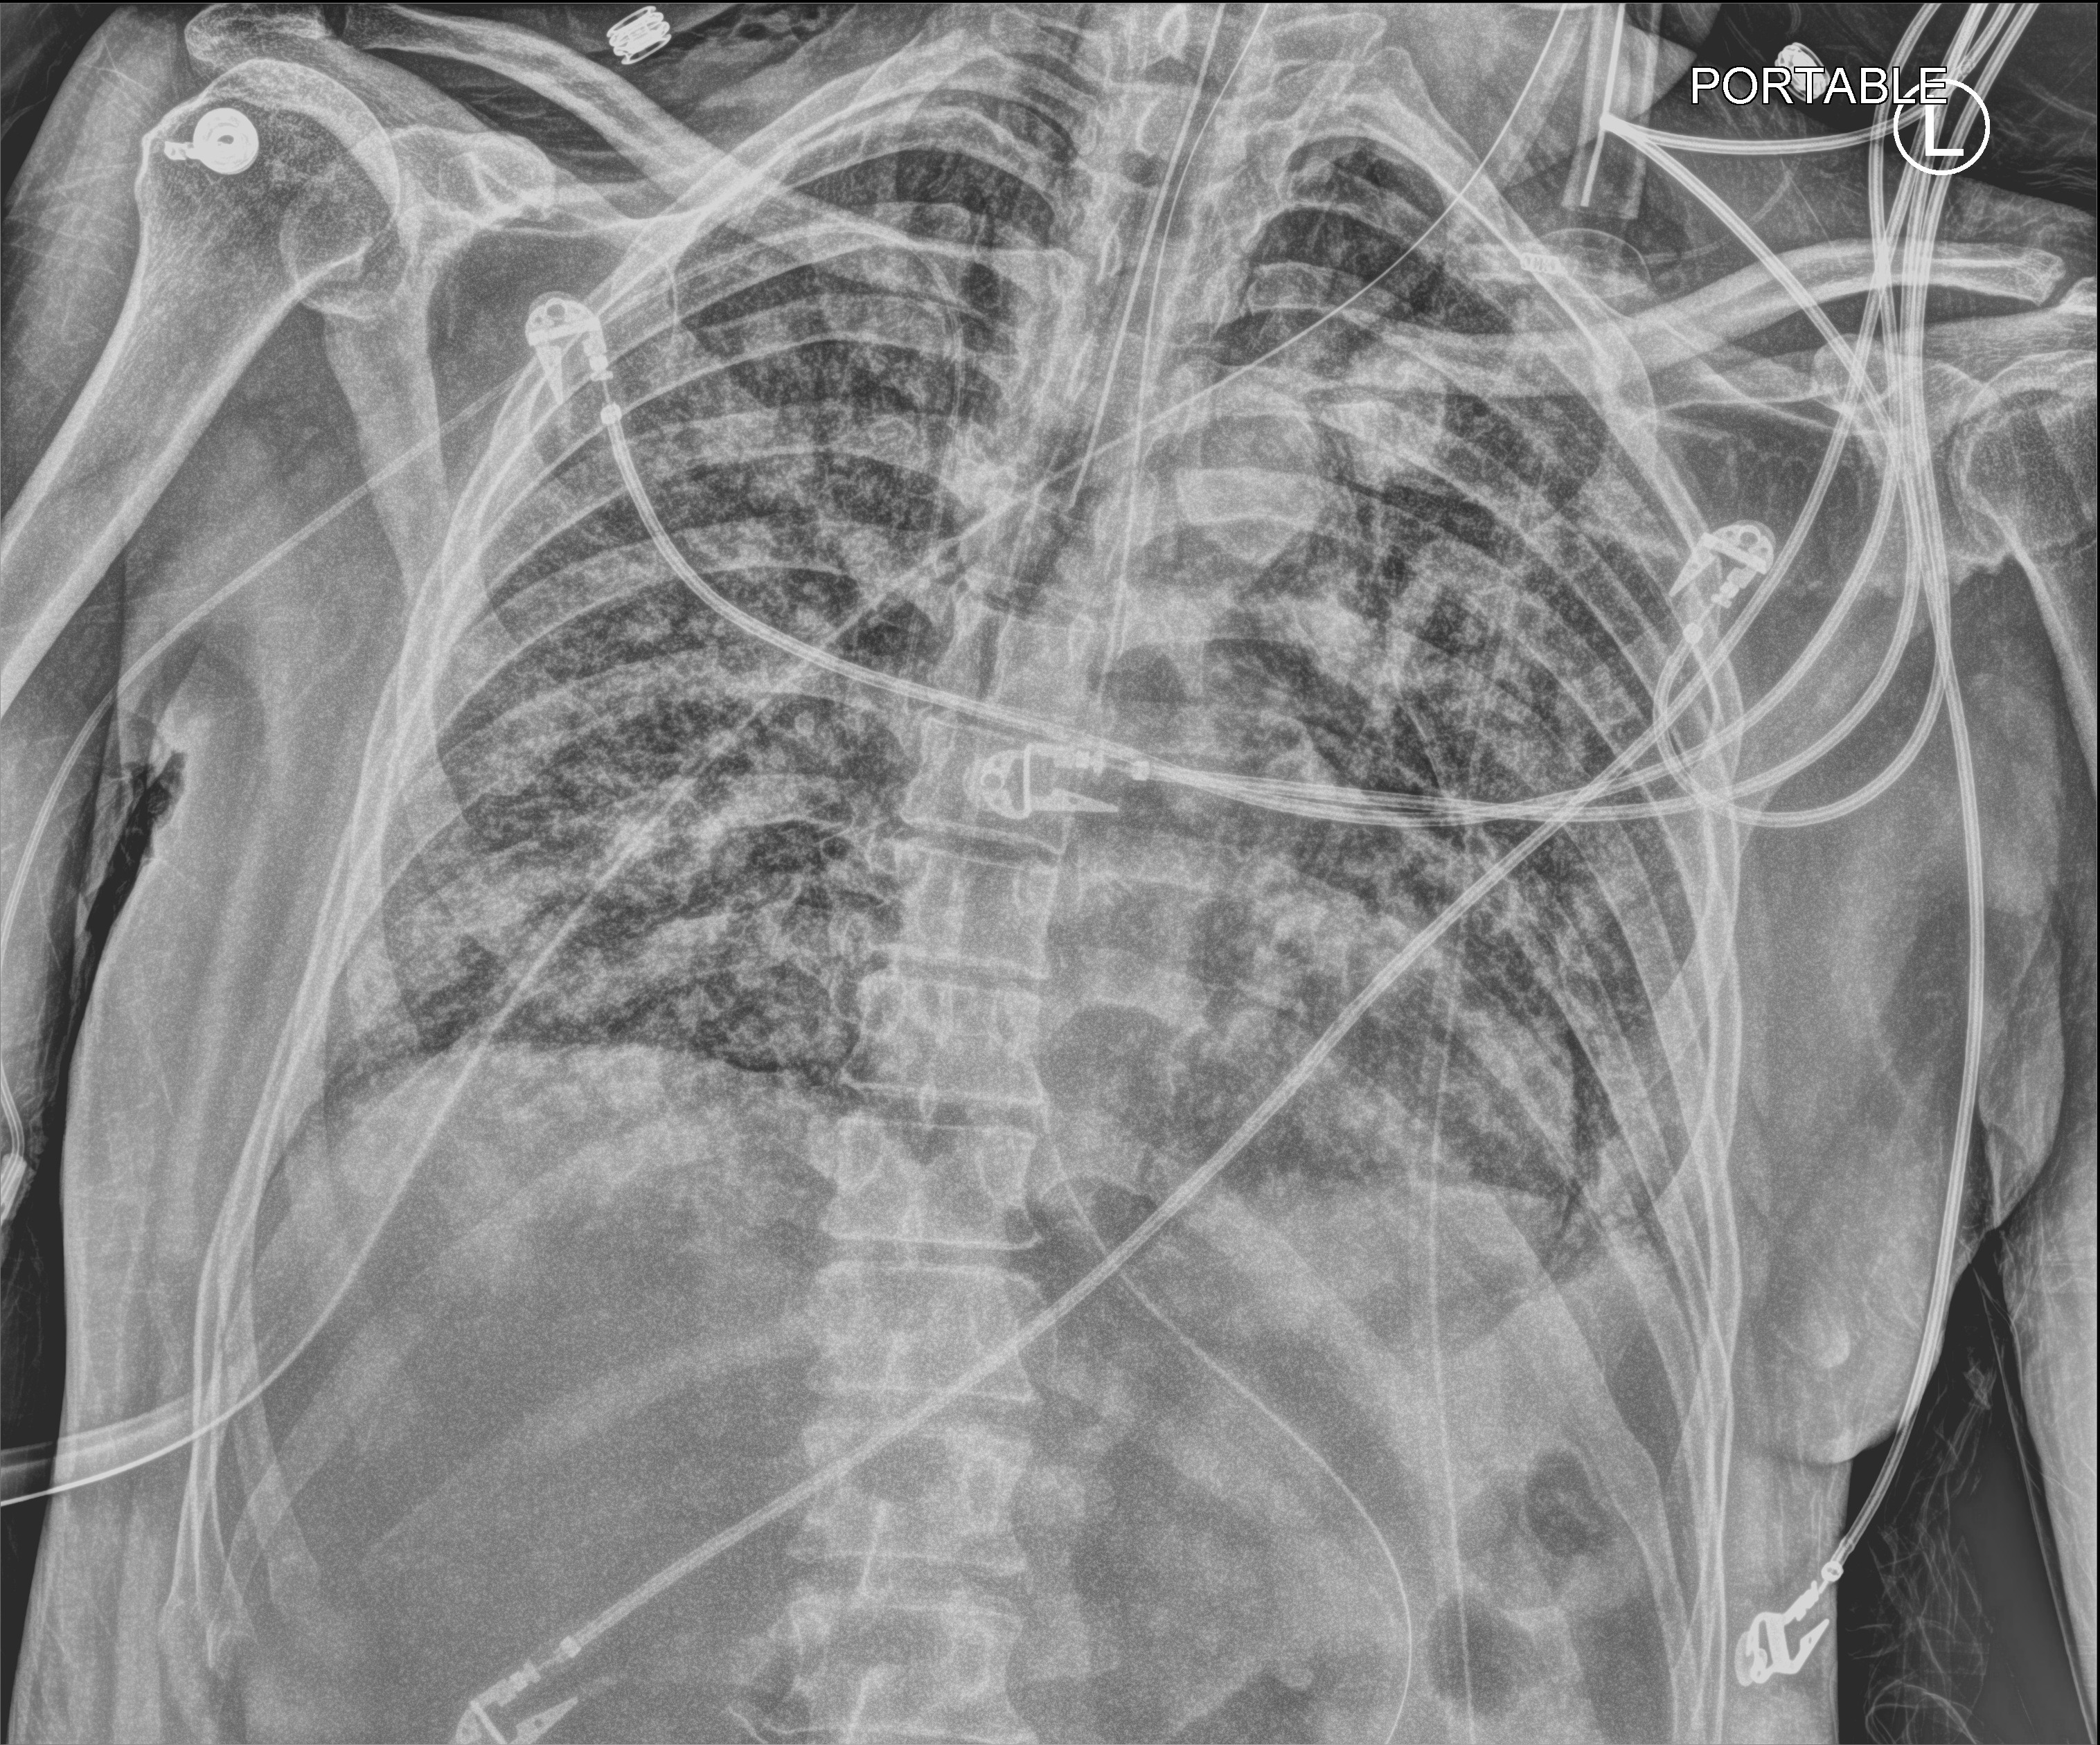
Bedside chest radiograph (computed radiography), anteroposterior (AP) projection. Patient hospitalised with COVID-19; male, aged 60–74 years.
From the hospital-stay record, not from the radiograph (when in the stay this image was taken is not recorded):
- admitted to intensive care during this hospital stay: yes
- other chronic lung disease (admission record): yes